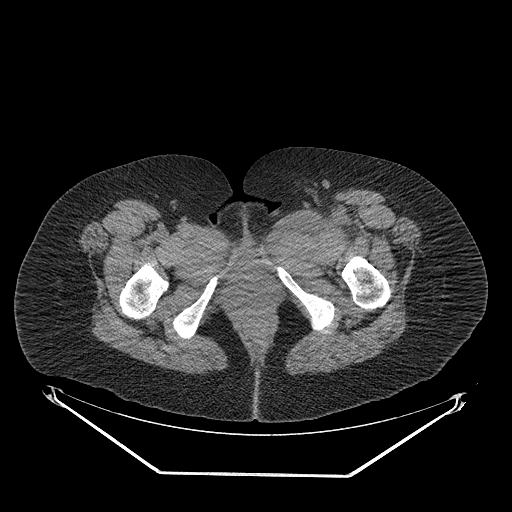
CT of an extremity soft-tissue mass (from a PET/CT study), one axial slice. Position 46 of 267 along the scan axis. Reconstruction kernel STANDARD. 140 kVp. Soft-tissue window (W 400 / L 40 HU). 3.75 mm slice thickness. 512 × 512 image matrix, field of view 500 × 500 mm. Female patient. From the clinical record (not read from this slice): histological type: myxofibrosarcoma; grade: intermediate; site of the primary tumour: left thigh.
Outlined on this slice (expert contour drawn on MRI and transferred to this co-registered scan by the dataset authors):
- gross tumour volume including surrounding oedema: bounding box [x1, y1, x2, y2] px = [265, 206, 366, 250]
- gross tumour volume (mass): [301, 206, 323, 225]